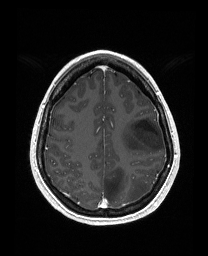
Brain MRI from a brain-tumour surgery series, one axial slice; slice 119 of 176 in the series (ordered by position); T1-weighted post-contrast; 1 mm slice thickness; 208 × 256 image matrix, field of view 203 × 250 mm. Case-level facts recorded for this patient, not image findings: histopathology: Astrocytoma; WHO grade: 3; IDH mutation: yes; tumour location: Left Frontal.
Structures marked on this image (manually delineated by an expert):
- tumour: bounding box [x1, y1, x2, y2] px = [120, 117, 164, 153]